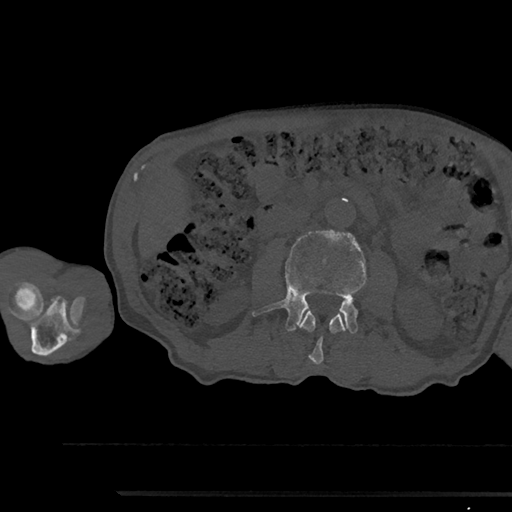
CT including the spine, one axial slice; position 519 of 797 along the scan axis; reconstruction kernel Br40s/3; 120 kVp; bone window (W 1800 / L 400 HU); 512 × 512 image matrix, field of view 367 × 367 mm. Patient: male, 79 years. From the clinical record (not read from this slice): primary cancer: prostate.
Structures marked on this image (semi-automatically segmented with operator editing):
- L2 vertebra: bounding box <299,310,347,364> (left, top, right, bottom; pixels)
- L3 vertebra: <252,230,367,333>